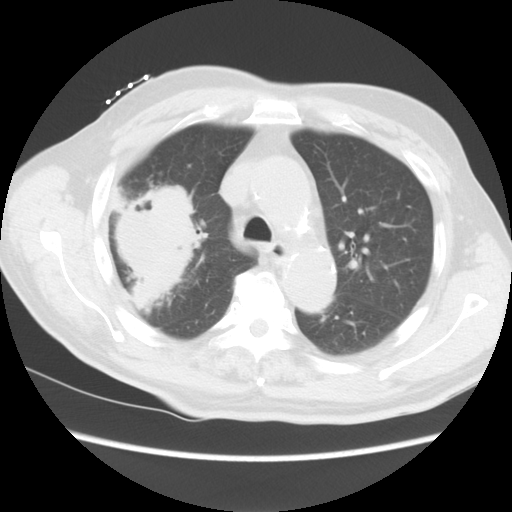
Chest CT, one axial slice; slice 12 of 15 in the series (ordered by position); reconstruction kernel STANDARD; 120 kVp; lung window (W 1500 / L -600 HU); 512 × 512 image matrix, field of view 350 × 350 mm. Patient: male, 68 years. From the clinical record (not read from this slice): clinical TNM (as recorded): T4 N3 M0.
Annotated regions visible in this slice (rectangle marked by the reading radiologist):
- lung tumour (recorded histology: squamous cell carcinoma): bounding box (x1, y1, x2, y2) in pixels: (114, 180, 198, 320)